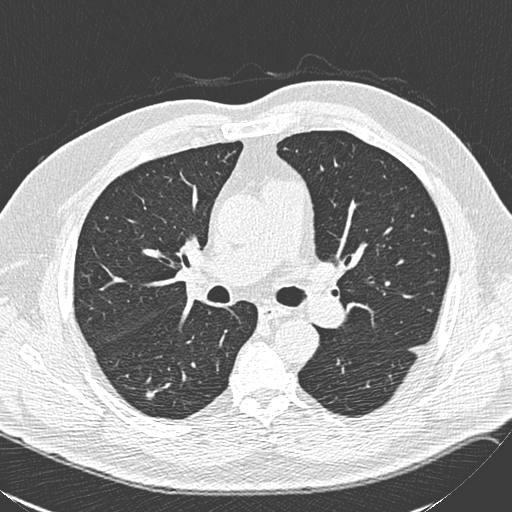
Low-dose screening chest CT, one axial slice; slice 155 of 248 in the series (ordered by position); lung window (W 1500 / L -600 HU); 512 × 512 image matrix, field of view 357 × 357 mm.
Outlined on this slice (outlined manually by an expert reader):
- lesion 1 (tumor, lower lobe of right lung): bounding box <147,392,154,398> (left, top, right, bottom; pixels)